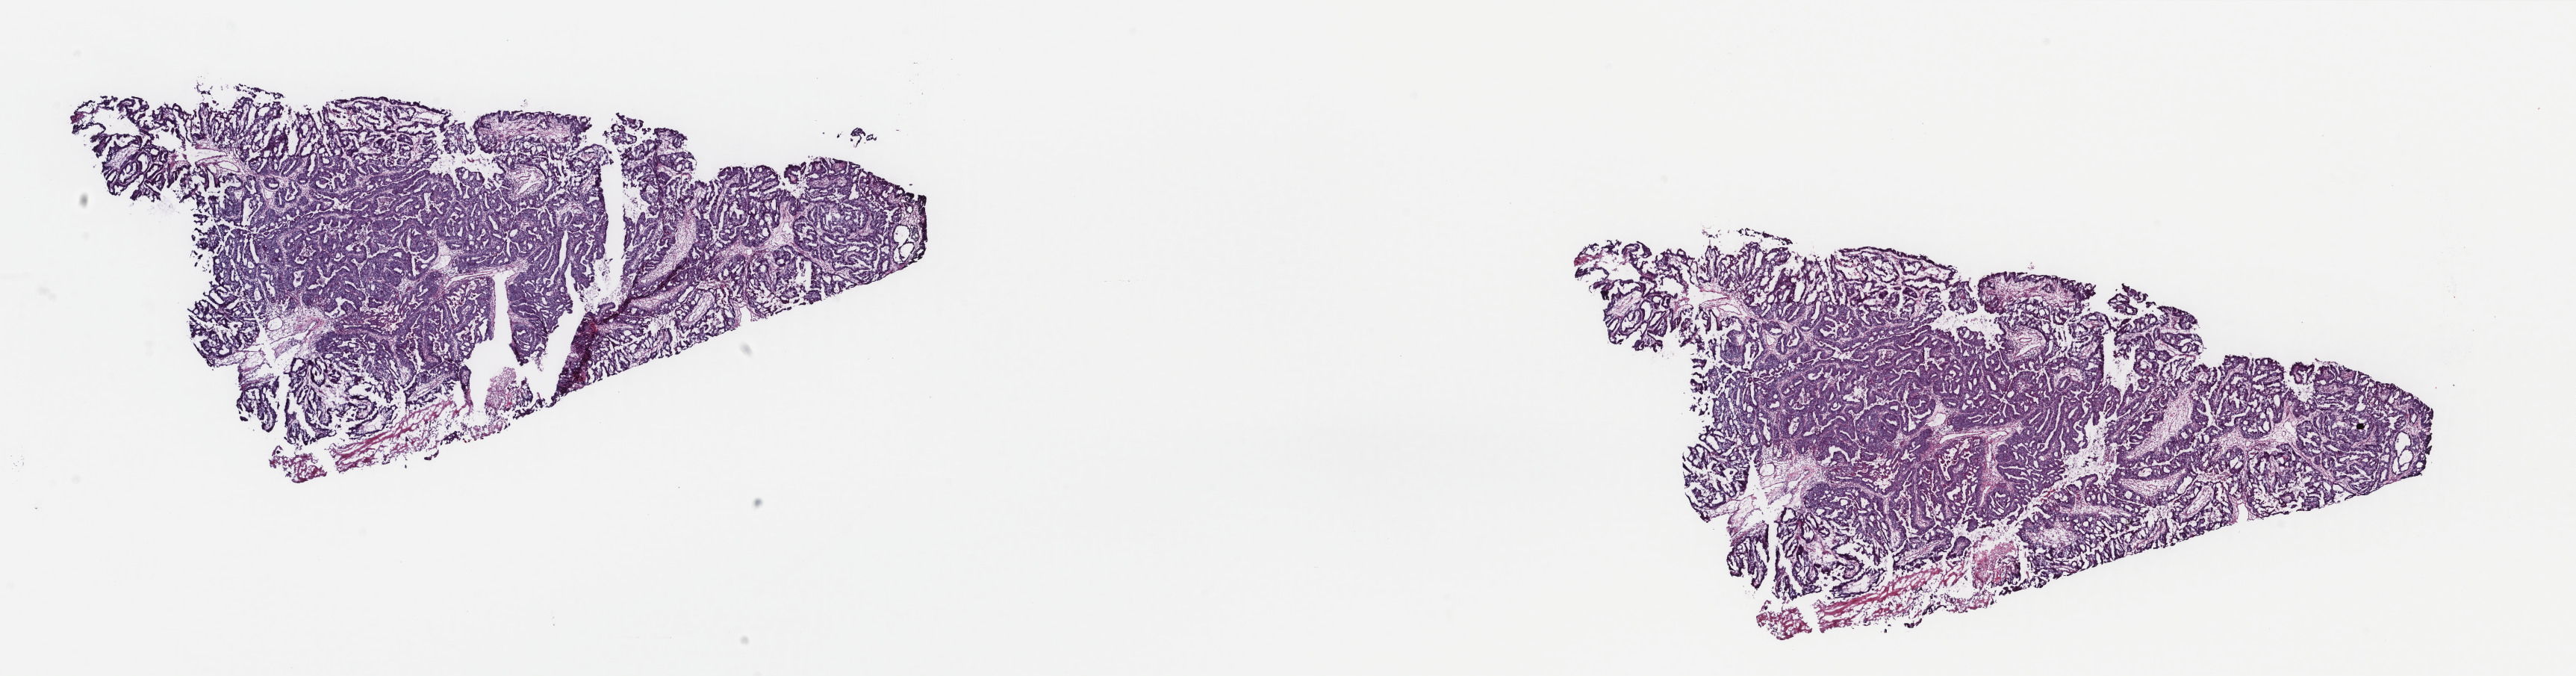
Digitized Hematoxylin and eosin (H&E) stained tissue section (whole slide), shown as a low-resolution overview of the whole scanned area (about 27.4 x 7.2 mm). Frozen section. Primary tumour sample from the uterus. Female patient; age at initial diagnosis 70 years. Histologic grade: G2 (moderately differentiated). Pathologist review of this section (percent, as recorded): tumour cells 82%, tumour nuclei 85%, normal cells 0%, stromal cells 15%, necrosis 3%. Infiltration values recorded for this section: lymphocyte infiltration 4%, monocyte infiltration 1%, neutrophil infiltration 3%.
Lymph nodes positive (case pathology): 0 of 52 examined. FIGO stage: IC. Histologic diagnosis: Endometrioid adenocarcinoma, NOS (endometrium).